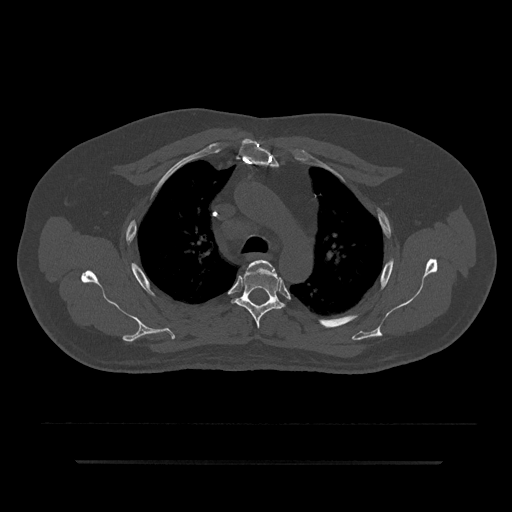
CT including the spine, one axial slice. Slice 619 of 797 in the series (ordered by position). 120 kVp. Bone window (W 1800 / L 400 HU). 0.5 mm slice thickness. 512 × 512 image matrix. Patient: male, 59 years. From the clinical record (not read from this slice): primary cancer: bile ducts; vertebrae with lytic lesions (as recorded): T10.
Structures marked on this image (semi-automatically segmented with operator editing):
- T3 vertebra: bounding box <248,260,275,272> (left, top, right, bottom; pixels)
- T4 vertebra: <232,266,285,328>